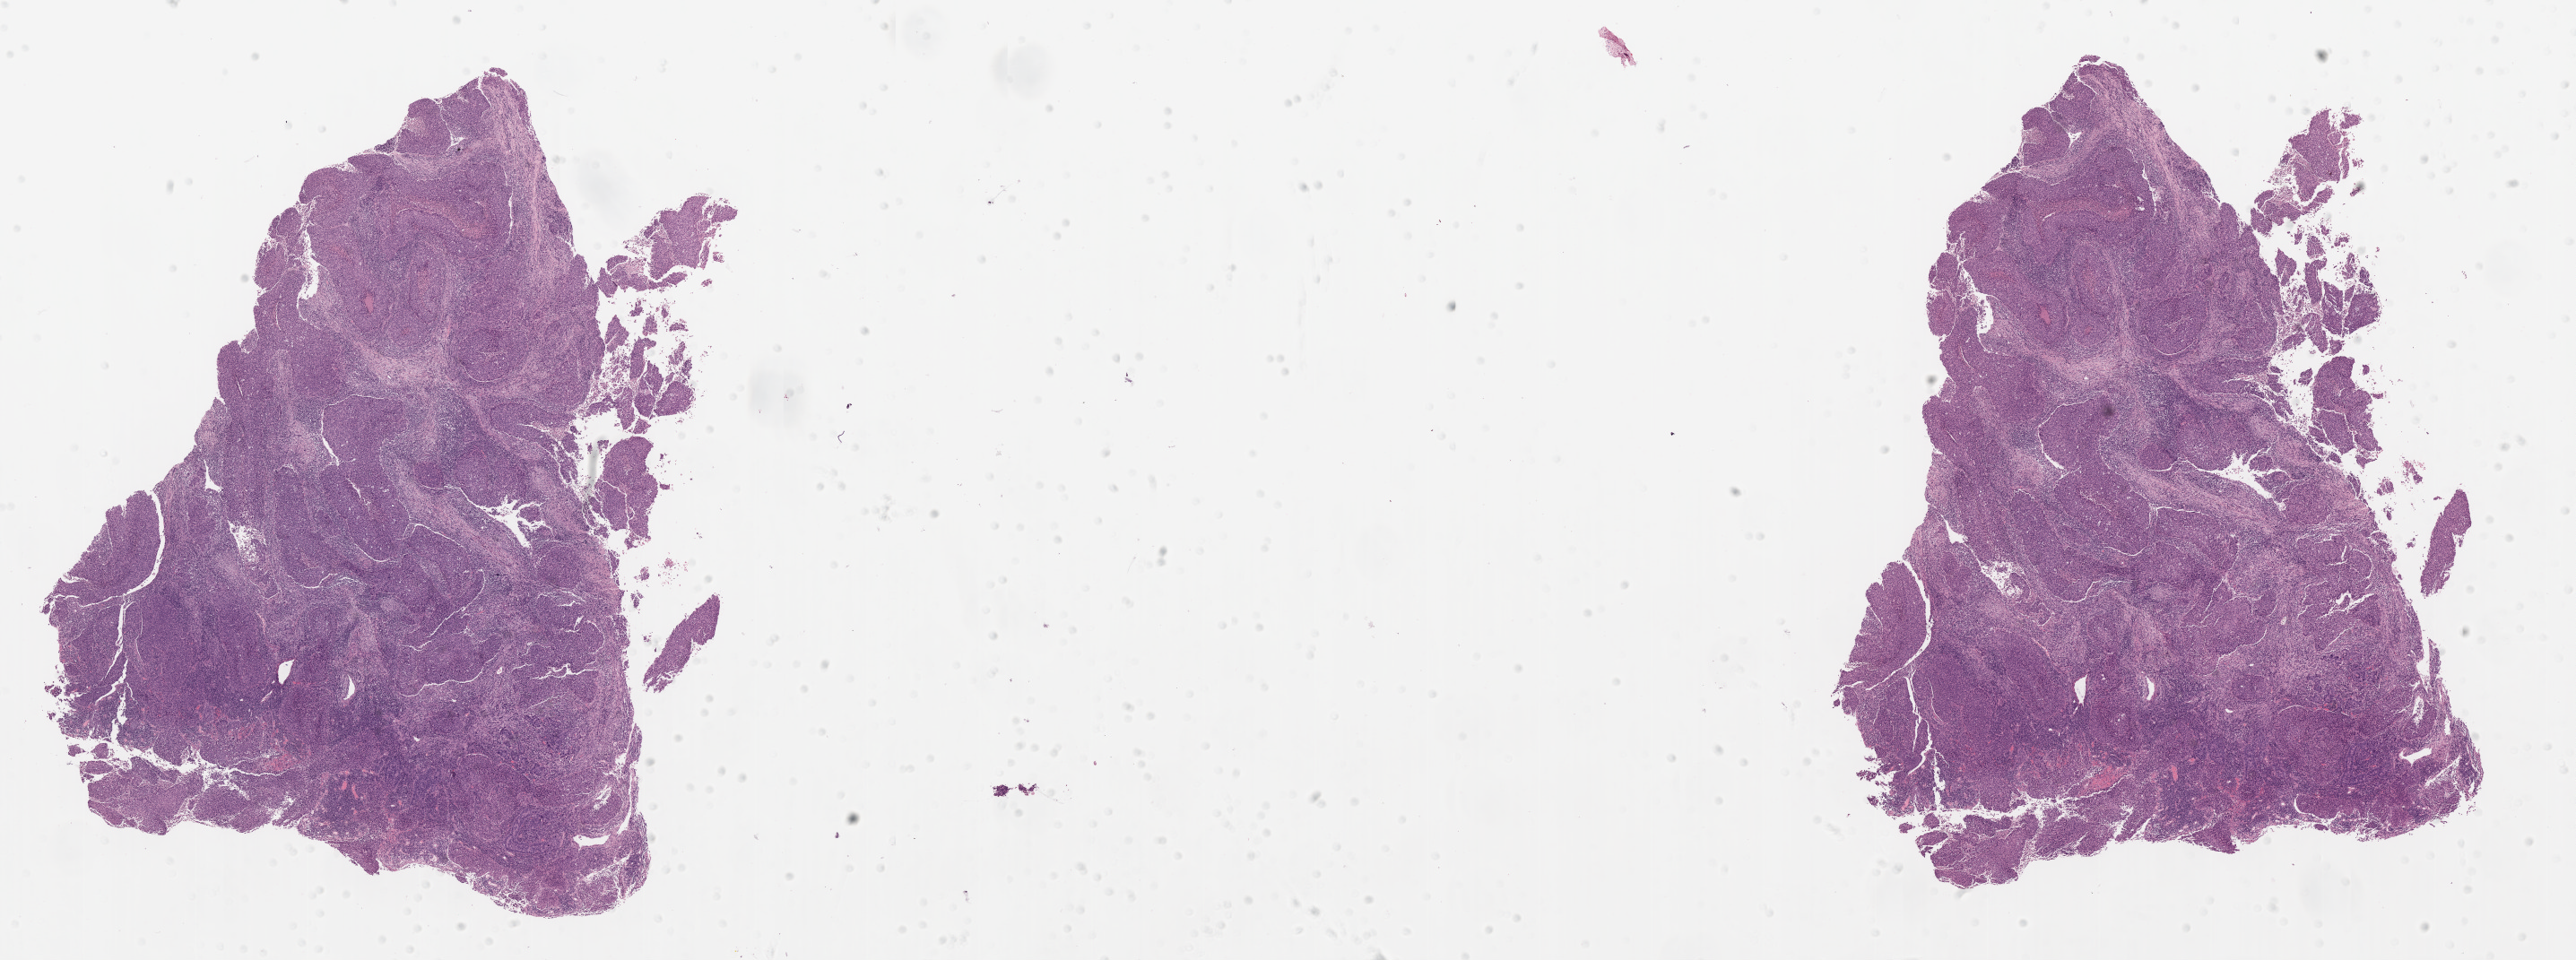
Whole-slide histology image, H&E, shown as a low-resolution overview of the whole scanned area (about 23.0 x 8.6 mm, acquisition: 20x scan), FFPE section, primary tumour sample from the cervix. Female patient; age at initial diagnosis 50 years.
Diagnosis: Squamous cell carcinoma, large cell, nonkeratinizing, NOS (cervix uteri).